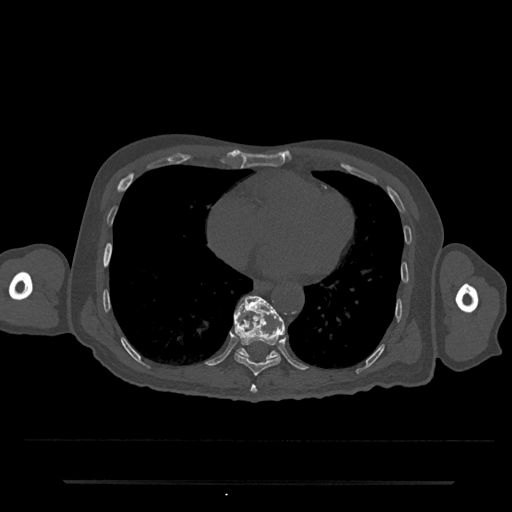
CT including the spine, one axial slice; position 351 of 797 along the scan axis; bone window (W 1800 / L 400 HU); 0.5 mm slice thickness; 512 × 512 image matrix. Patient: male, 74 years. Case-level facts recorded for this patient, not image findings: primary cancer: prostate.
Outlined on this slice (semi-automatically segmented with operator editing):
- T10 vertebra: bounding box <236,295,285,361> (left, top, right, bottom; pixels)
- T8 vertebra: <250,385,257,393>
- T9 vertebra: <234,296,285,376>